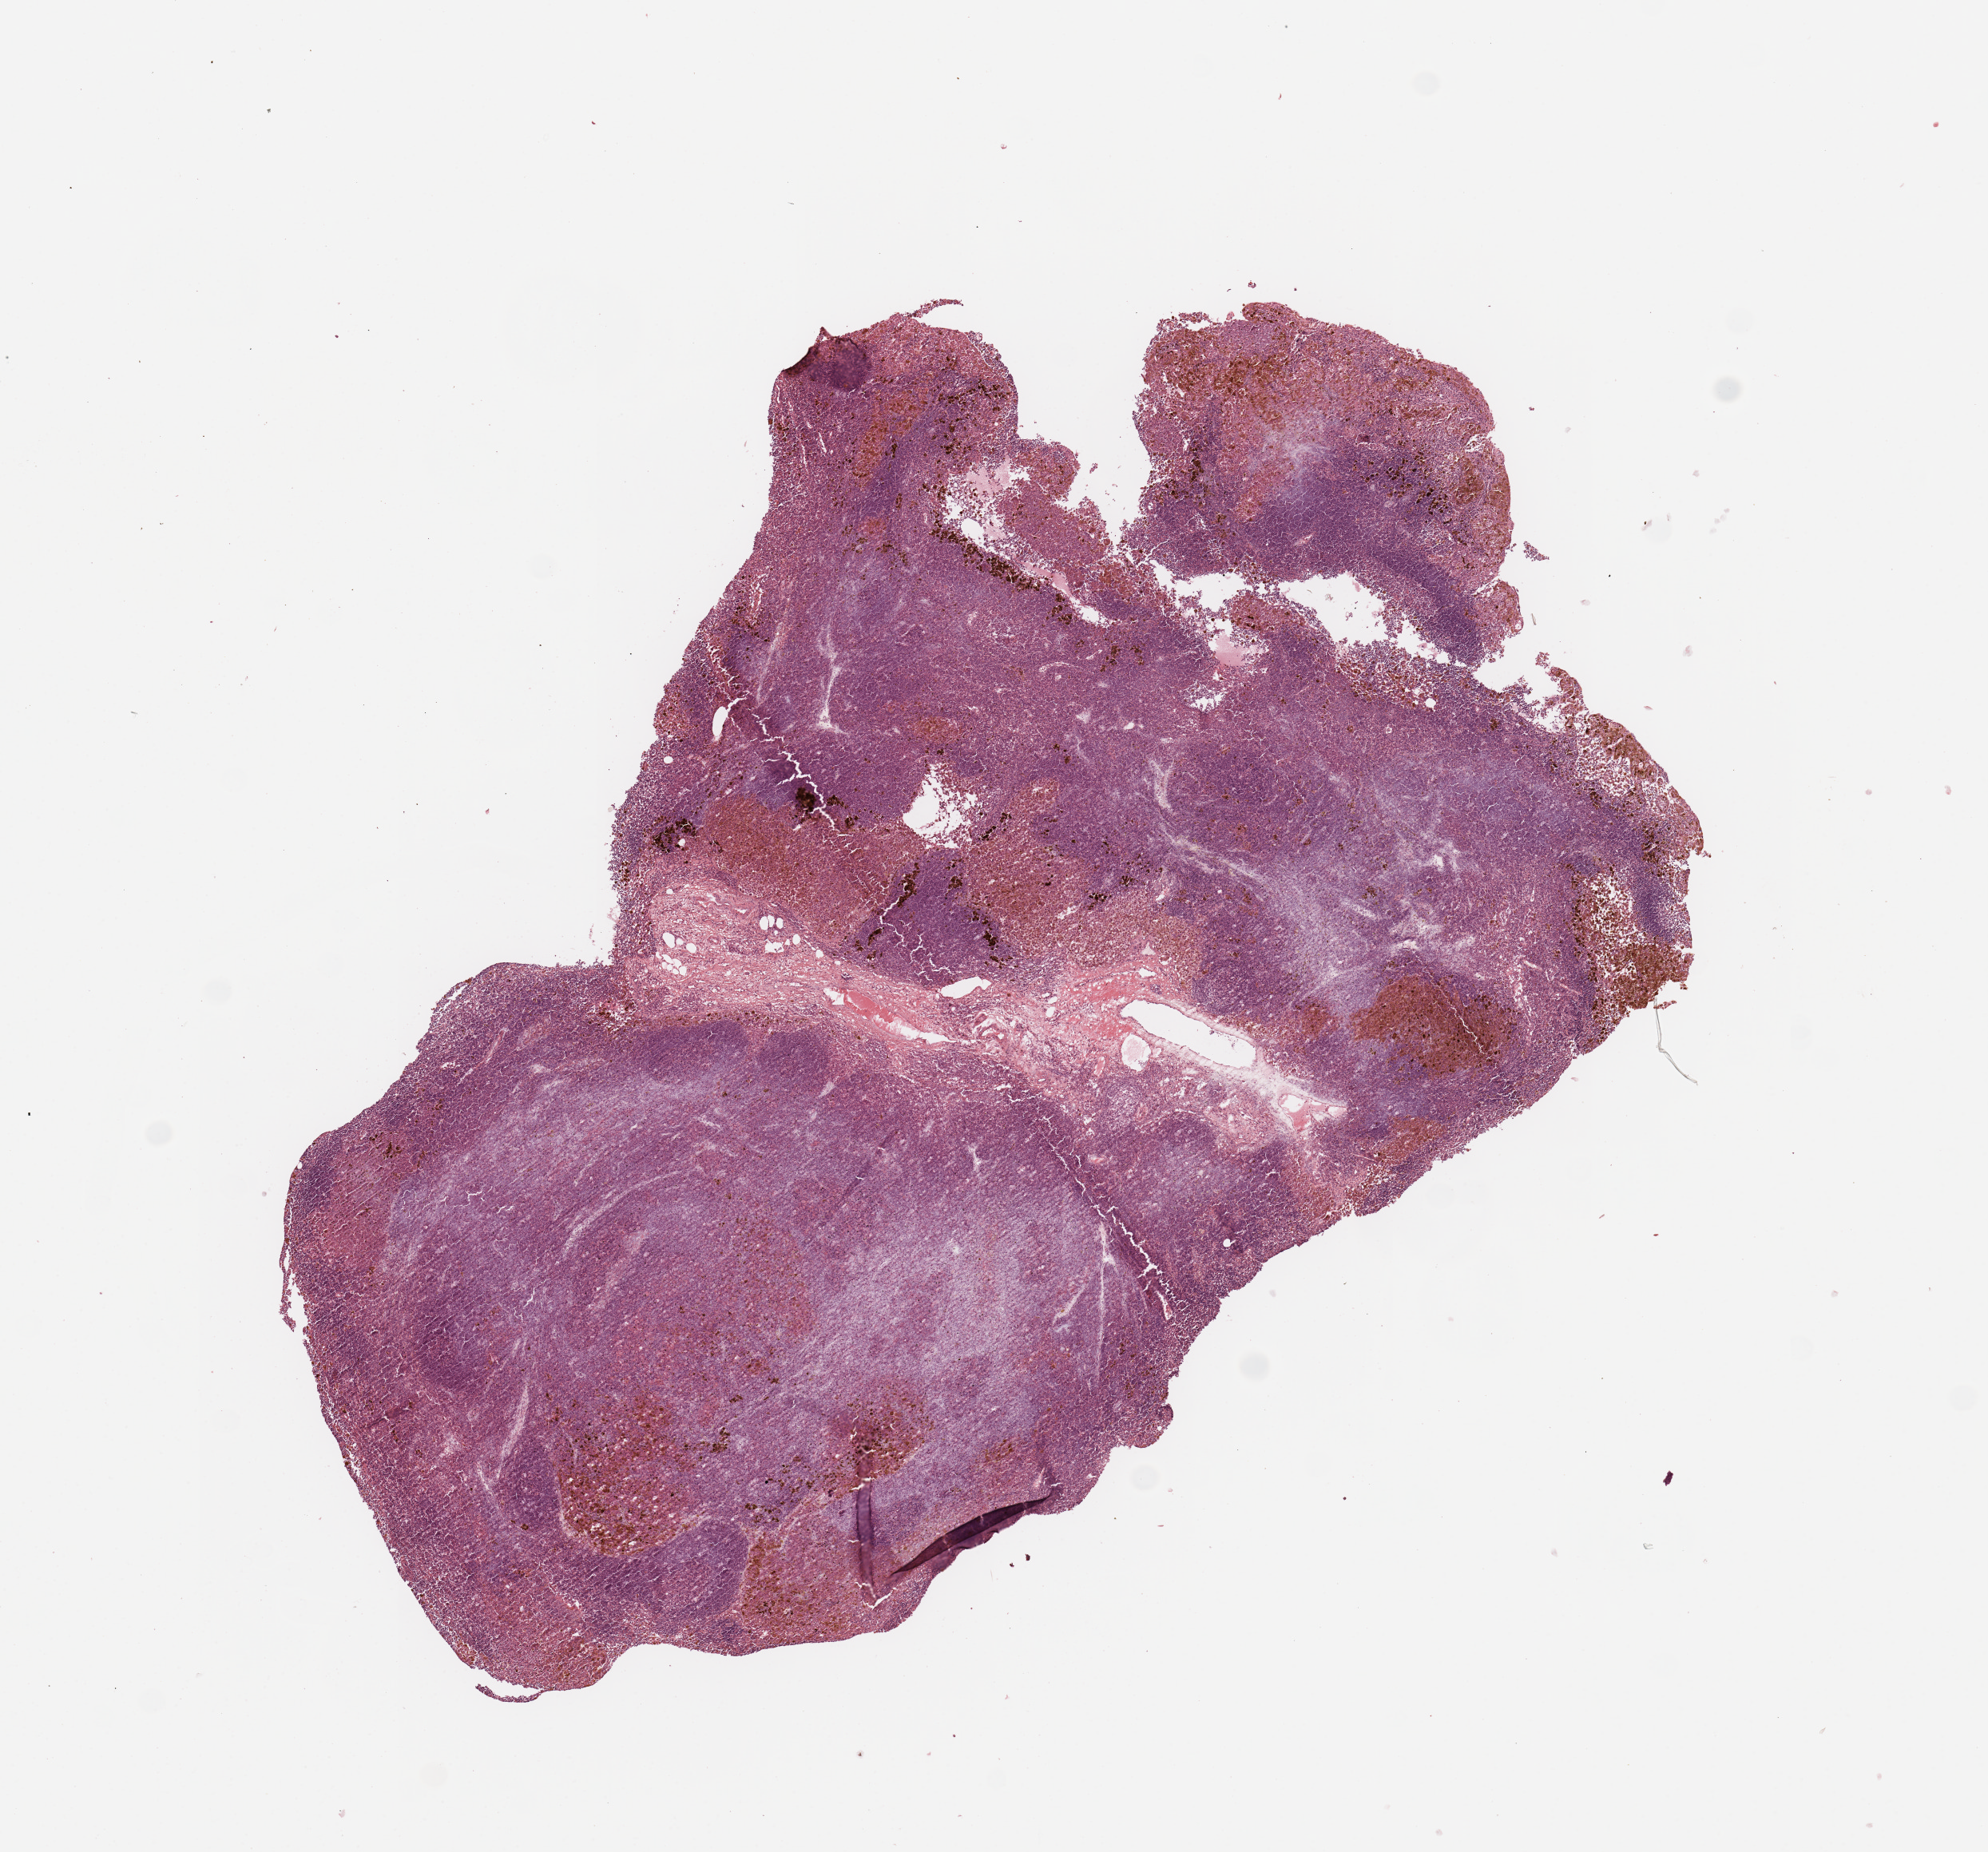
Digitized Hematoxylin and eosin (H&E) stained tissue section (whole slide), a low-resolution overview of the entire scanned area, about 9.8 x 9.2 mm (acquisition: 20x scan); melanoma tumour tissue; sampled site not recorded. 44-year-old female patient.
- patient diagnosis (cohort enrolment): cutaneous melanoma (skin)
- primary tumour site (as recorded): trunk